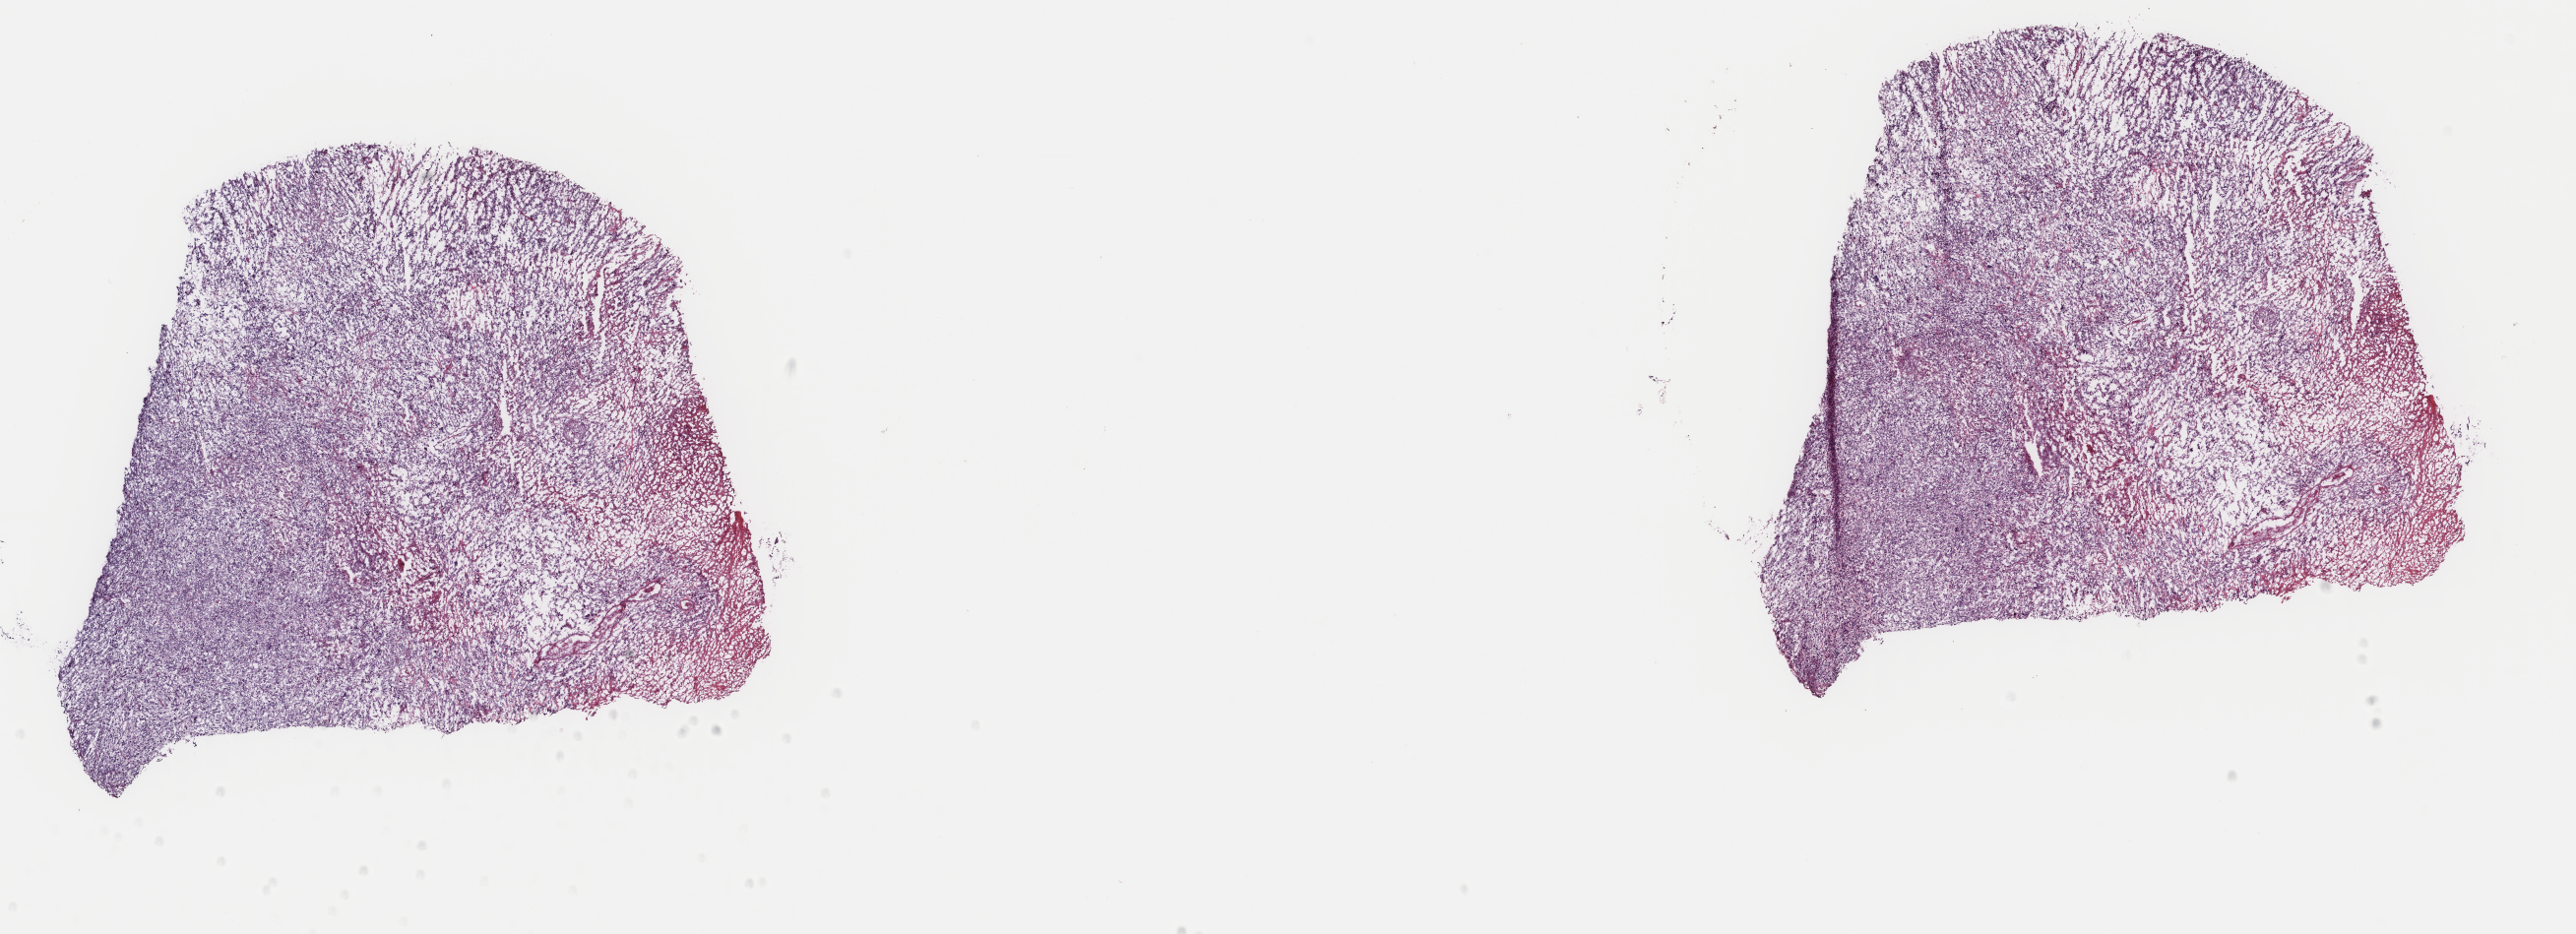
Digitized Hematoxylin and eosin (H&E) stained tissue section (whole slide) — a low-resolution overview of the entire scanned area, about 20.8 x 7.5 mm (slide scanned at 40x), frozen section from the top of the tissue portion, esophagus, primary tumour sample. Male, age 49 years at initial diagnosis. Histologic grade: G3 (poorly differentiated). Composition of this section per pathologist review: tumour cells 90%, tumour nuclei 95%, normal cells 0%, stromal cells 0%, necrosis 10%. Infiltration values recorded for this section: lymphocyte infiltration 0%, monocyte infiltration 0%, neutrophil infiltration 0%.
Histologic diagnosis: Squamous cell carcinoma, NOS (lower third of esophagus). AJCC pathologic stage: III. TNM: T3 N1 M0. Lymph nodes positive (case pathology): 8 of 35 examined.